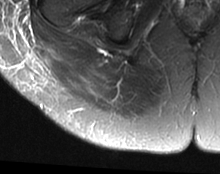
MRI of an extremity soft-tissue mass, one axial slice; position 11 of 63 along the scan axis; T2-weighted fat-saturated; MR volume resampled by the dataset authors to the PET/CT grid (not the native acquisition matrix); 3.27 mm slice thickness; 220 × 174 image matrix. Female patient. Case-level facts recorded for this patient, not image findings: histological type: spindle cell suggestive of myxofibrosarcoma; grade: intermediate; site of the primary tumour: right buttock.
Annotated regions visible in this slice (expert contour drawn on MRI and transferred to this co-registered scan by the dataset authors):
- gross tumour volume (mass): bounding box <47,47,59,64> (left, top, right, bottom; pixels)